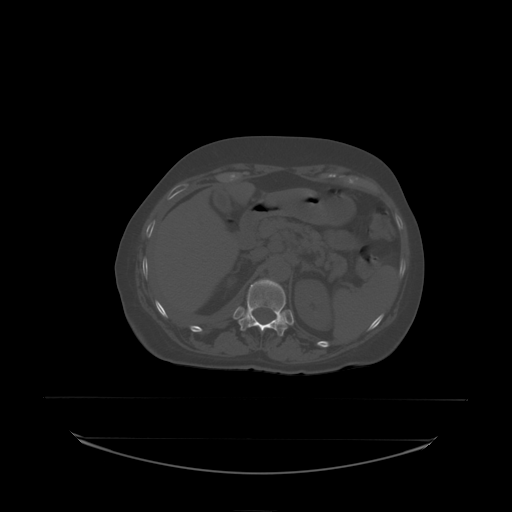
CT including the spine, one axial slice; position 94 of 242 along the scan axis; bone window (W 1800 / L 400 HU); 2.5 mm slice thickness; 512 × 512 image matrix. Patient: female, 53 years. Case-level facts recorded for this patient, not image findings: primary cancer: lung; vertebrae with lytic lesions (as recorded): T7, L1.
Structures marked on this image (semi-automatically segmented with operator editing):
- T12 vertebra: bounding box (x1, y1, x2, y2) in pixels: (238, 279, 288, 335)